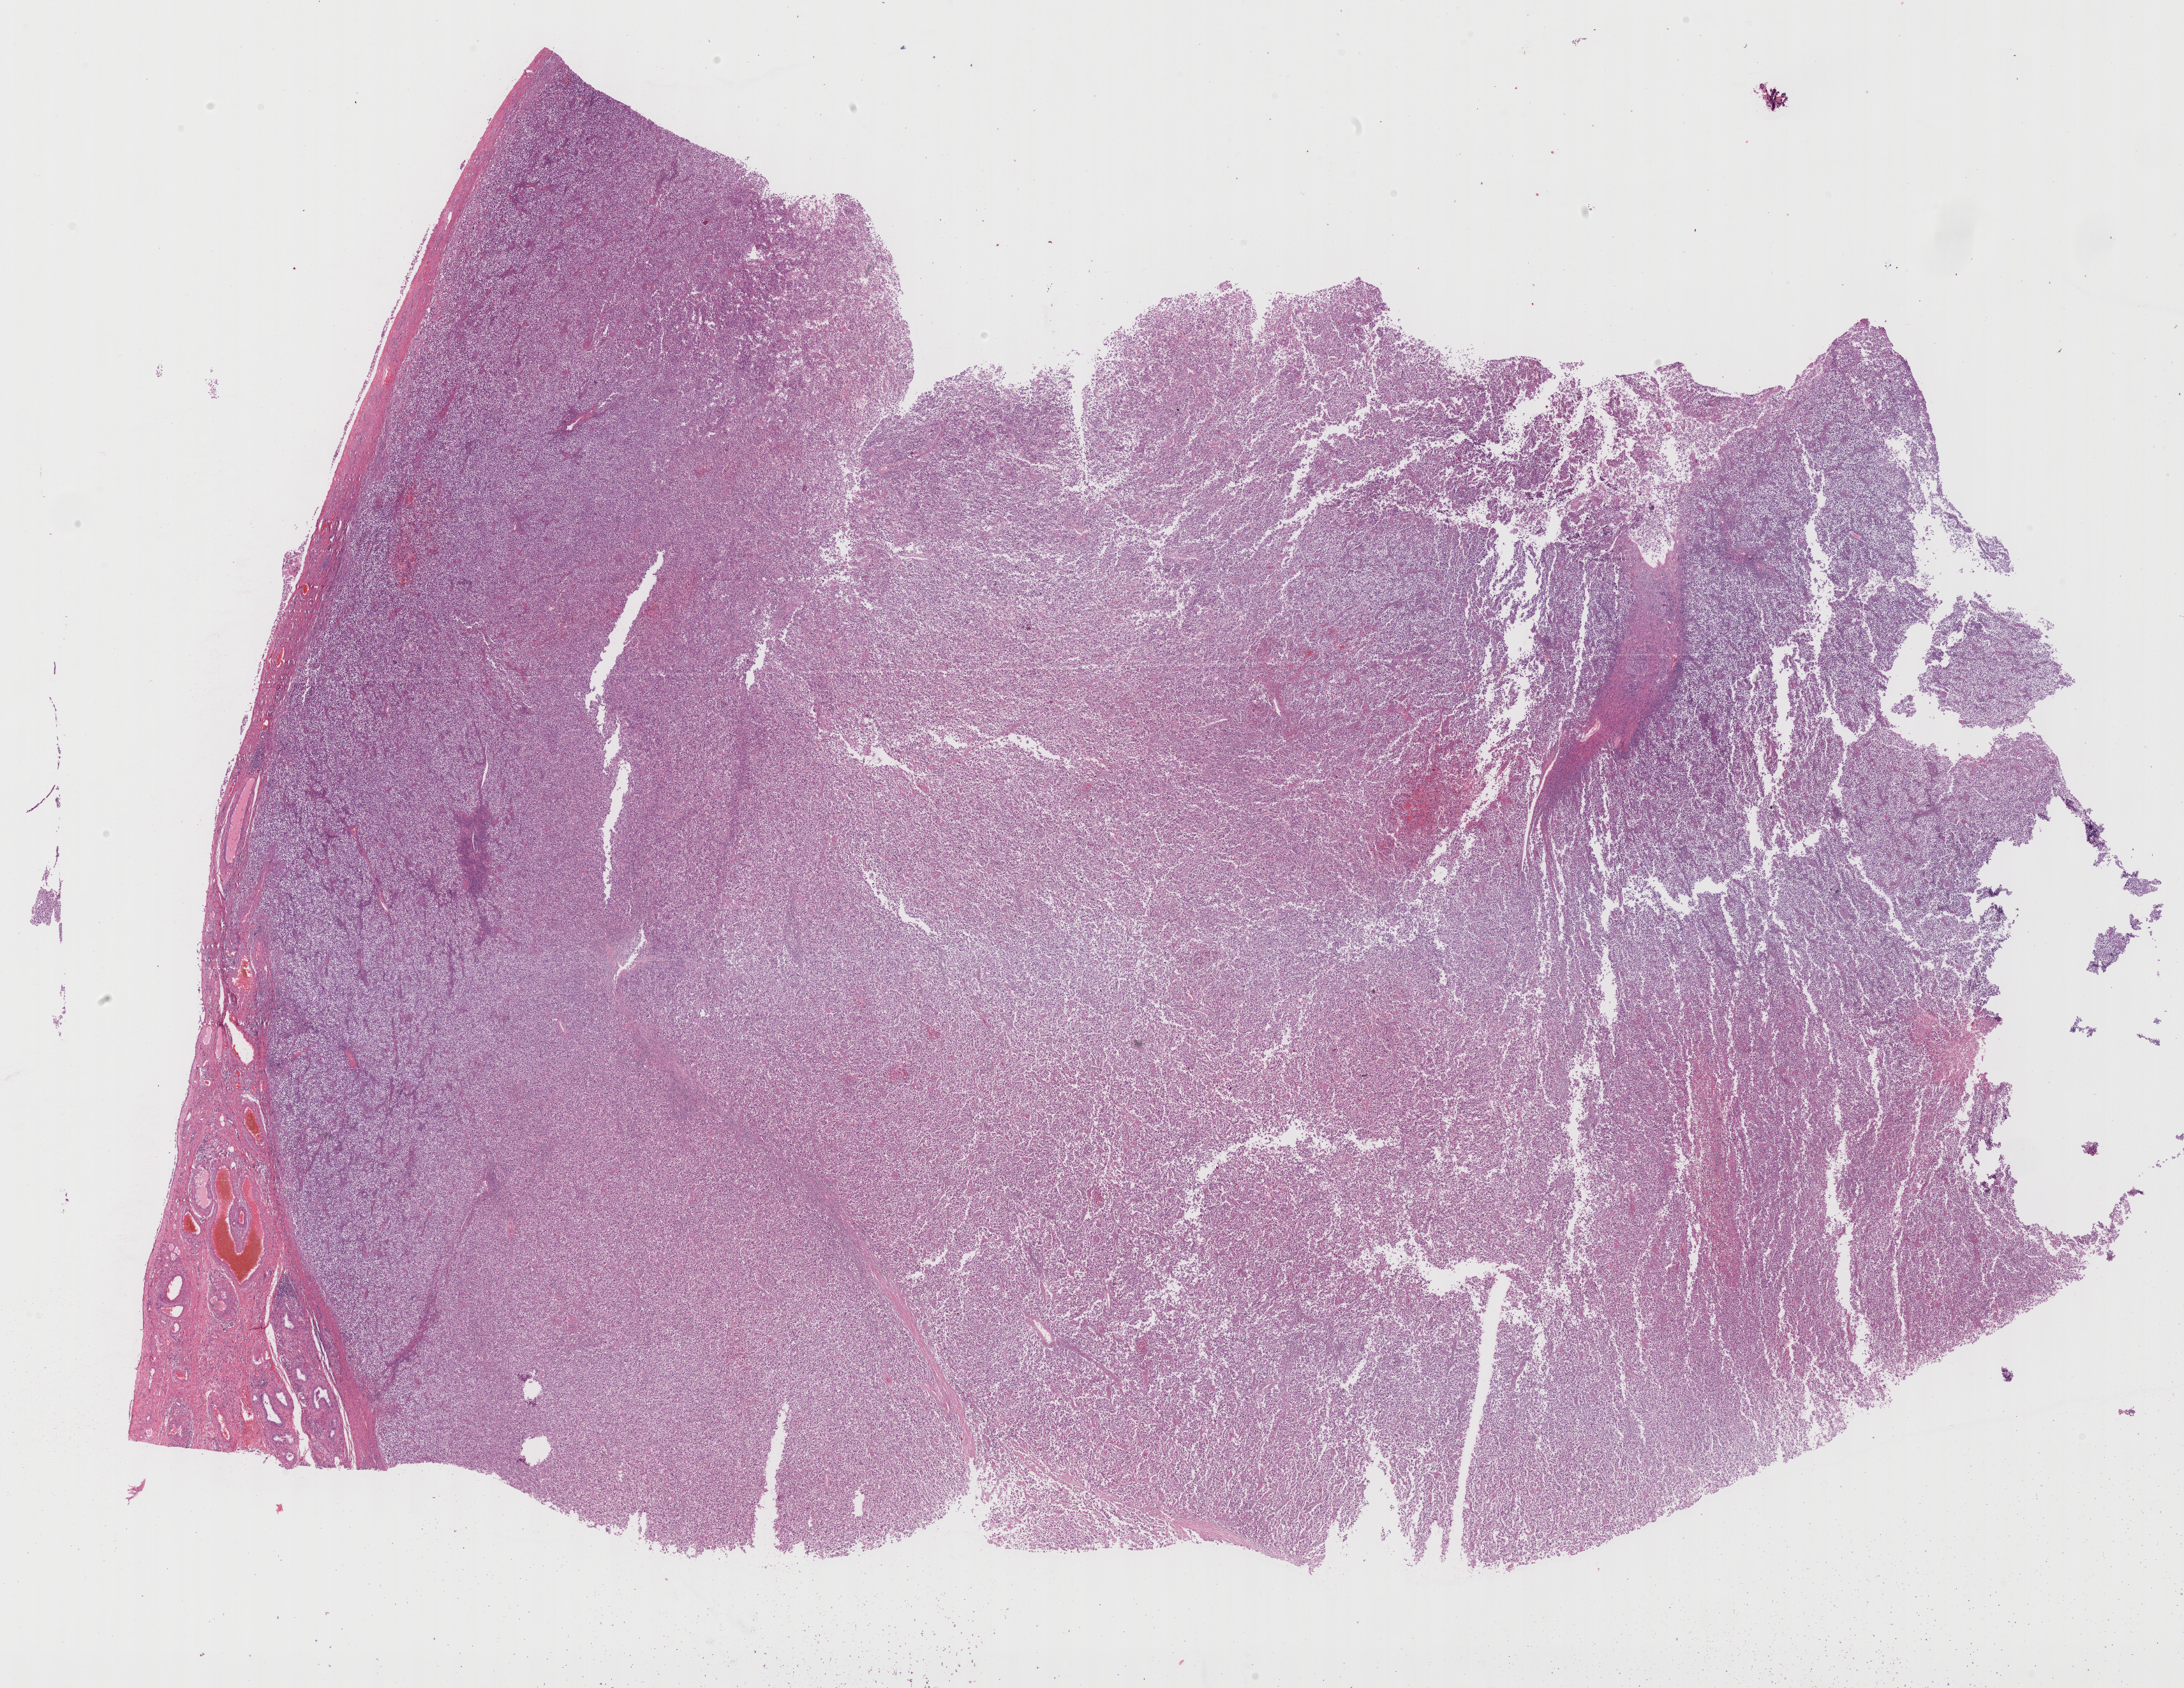
Hematoxylin and eosin (H&E) stained whole-slide image, low-resolution overview of the scanned area, about 27.7 x 21.4 mm; formalin-fixed paraffin-embedded (FFPE) diagnostic section; testis, primary tumour sample. Male patient; age at initial diagnosis 47 years.
- diagnosis: Seminoma, NOS
- laterality: left
- AJCC pathologic stage: IA (6th edition)